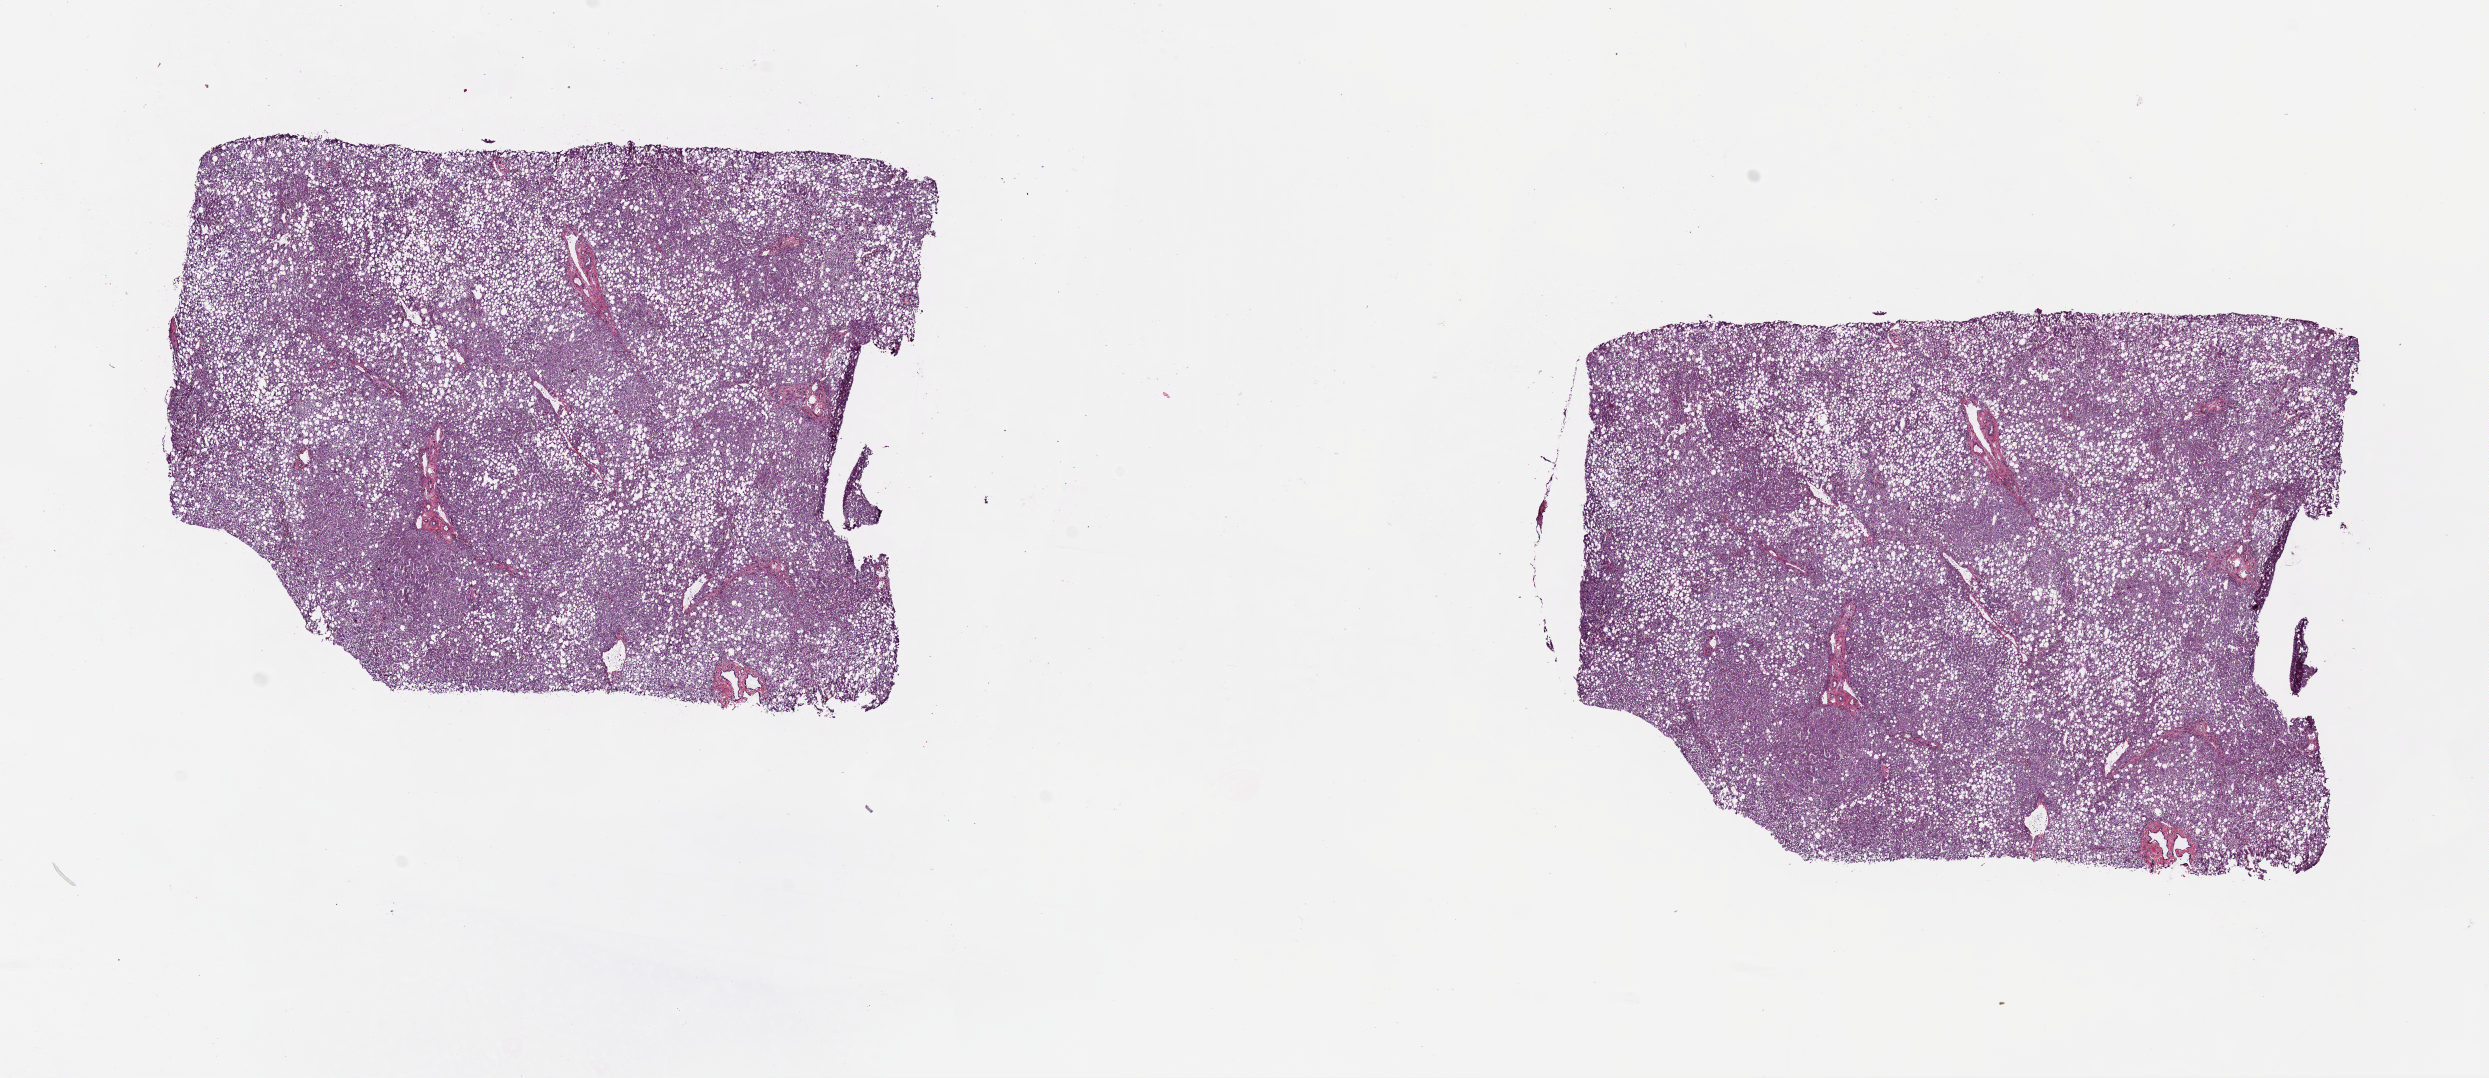
H&E whole-slide image — shown as a low-resolution overview of the whole scanned area (about 19.6 x 8.5 mm), frozen section from the top of the tissue portion, solid tissue normal (non-tumour tissue) sample from the liver. Male patient; age at initial diagnosis 67 years. Composition of this section per pathologist review: tumour cells 0%, tumour nuclei 0%, normal cells 100%, stromal cells 0%, necrosis 0%. Inflammatory infiltration, as recorded: lymphocyte infiltration 6%, monocyte infiltration 2%, neutrophil infiltration 0%.
This section: solid tissue normal (non-tumour) sample from the same patient. Patient diagnosis: Hepatocellular carcinoma, NOS.